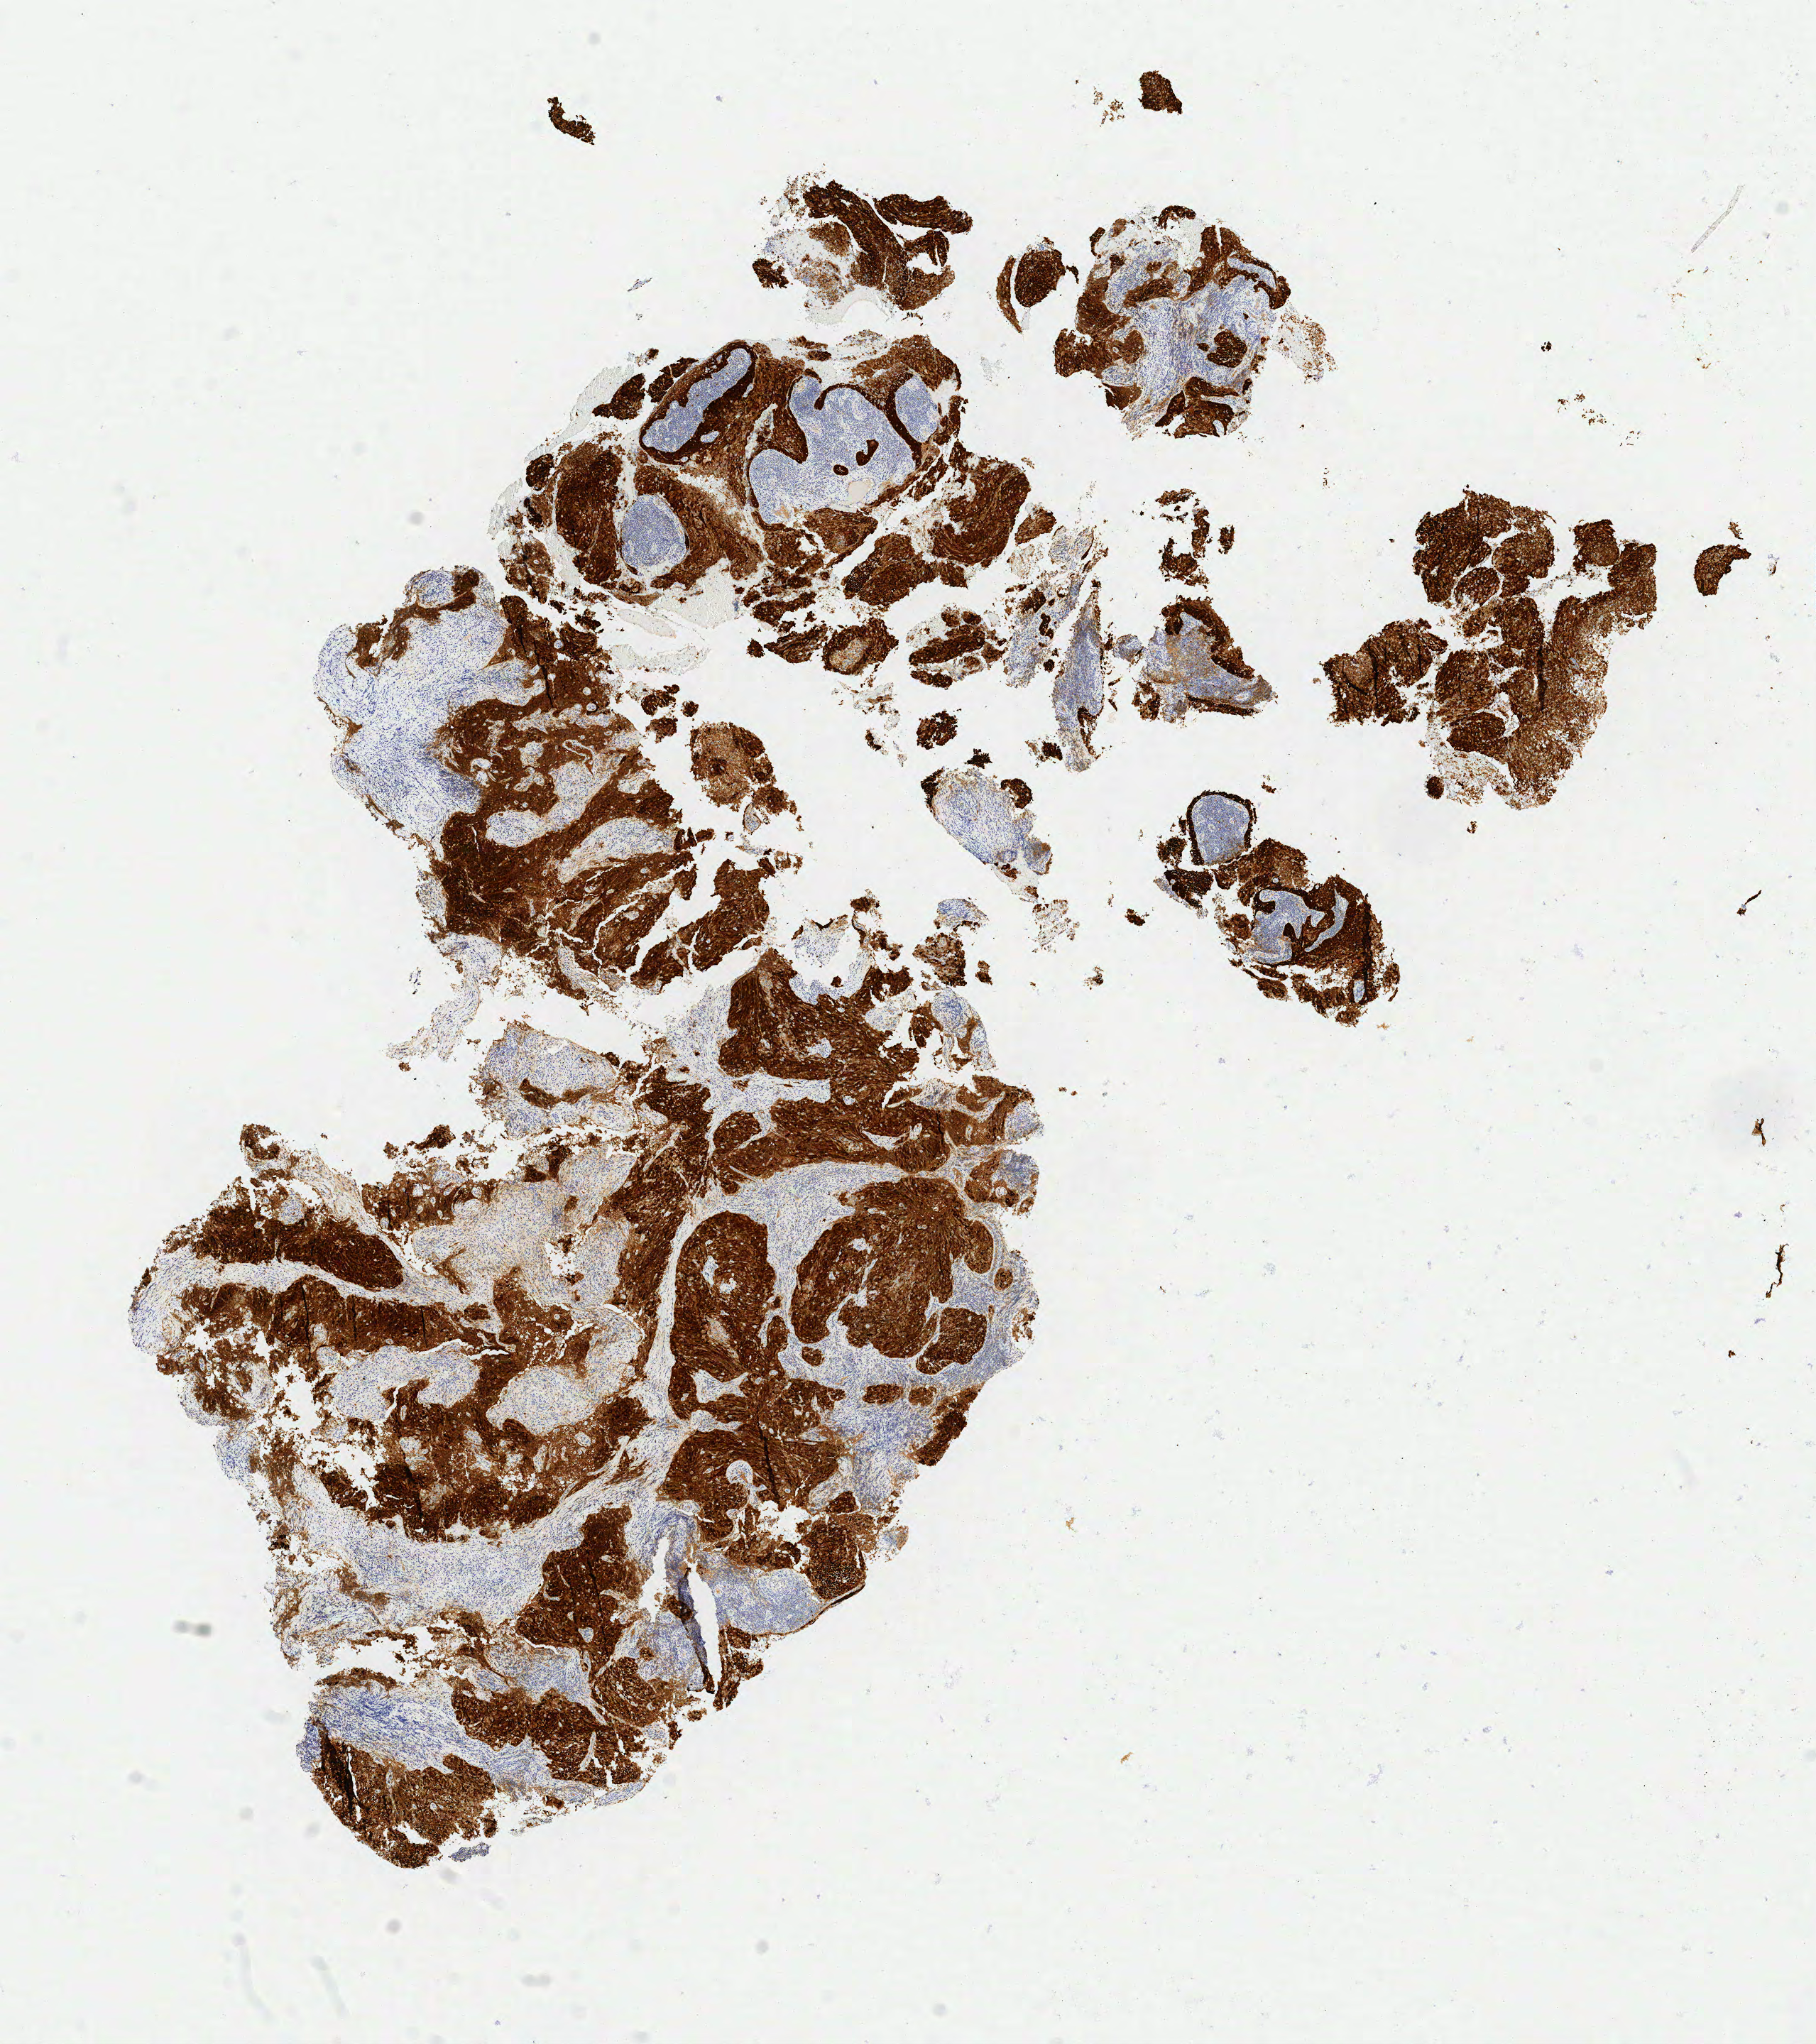
IHC for p16 (p16INK4a), whole-slide image — low-resolution overview of the scanned area, about 10.2 x 11.5 mm; specimen: tumor tissue; anatomic site: cervix. Patient: female, aged 50.
Diagnosis: Squamous cell carcinoma, large cell, nonkeratinizing, NOS.